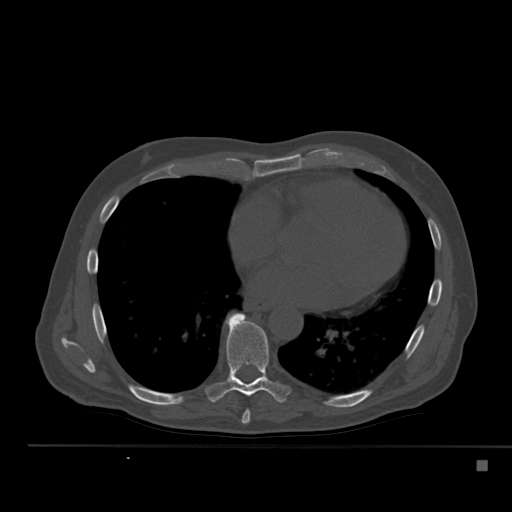
CT including the spine, one axial slice; 120 kVp; bone window (W 1800 / L 400 HU); 1.5 mm slice thickness; 512 × 512 image matrix, field of view 408 × 408 mm. Male patient, age 70 years. Case-level facts recorded for this patient, not image findings: primary cancer: renal; vertebrae with lytic lesions (as recorded): T4, T6, T10, T12, L3, L4, L5.
Structures marked on this image (semi-automatically segmented with operator editing):
- T7 vertebra: bounding box (x1, y1, x2, y2) in pixels: (241, 410, 250, 424)
- T8 vertebra: (206, 313, 290, 403)